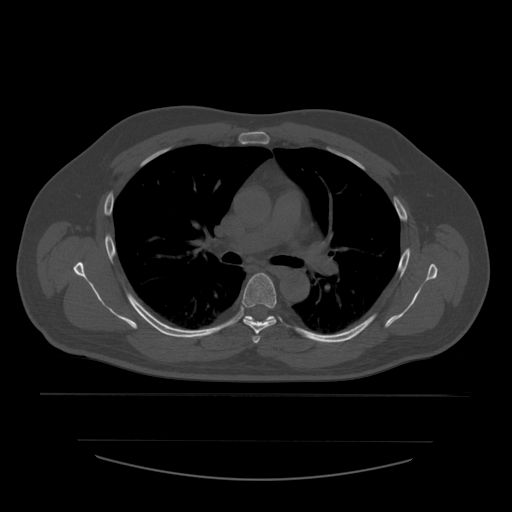
CT including the spine, one axial slice. Slice 395 of 532 in the series (ordered by position). Reconstruction kernel STANDARD. 120 kVp. Bone window (W 1800 / L 400 HU). 512 × 512 image matrix, field of view 441 × 441 mm. Patient age 44 years. From the clinical record (not read from this slice): primary cancer: soft tissue sarcoma.
Structures marked on this image (semi-automatically segmented with operator editing):
- T4 vertebra: box from (x=253, y=336) to (x=261, y=344) px
- T5 vertebra: (x=242, y=273)–(x=277, y=334)
- T6 vertebra: (x=245, y=316)–(x=274, y=322)